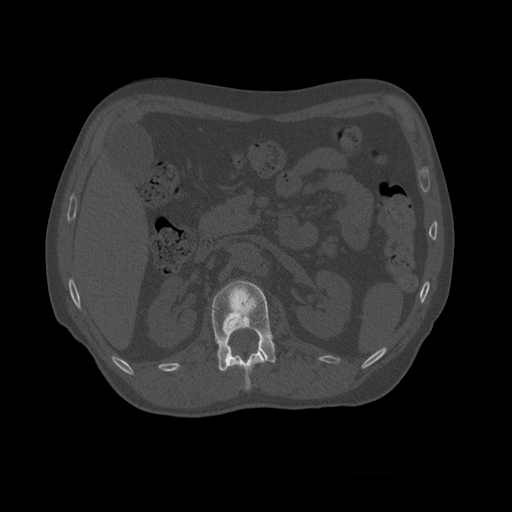
CT including the spine, one axial slice; slice 362 of 450 in the series (ordered by position); 120 kVp; bone window (W 1800 / L 400 HU); 1.25 mm slice thickness; 512 × 512 image matrix, field of view 405 × 405 mm. Patient age 75 years. From the clinical record (not read from this slice): primary cancer: prostate.
Structures marked on this image (semi-automatic segmentation, software-assisted and operator-edited):
- L1 vertebra: bounding box [x1, y1, x2, y2] px = [212, 280, 276, 372]
- T10 vertebra: [222, 344, 267, 371]
- T11 vertebra: [226, 350, 266, 391]